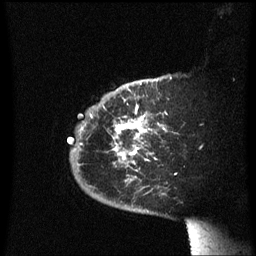
Breast MRI (dynamic contrast-enhanced), one sagittal slice. Position 48 of 60 along the scan axis. Dynamic contrast-enhanced series, image 2 of 3 at this slice position (ordered by acquisition). 1.5 T. TE 4.2 ms, TR 8.4 ms. 256 × 256 image matrix, field of view 200 × 200 mm. Patient: female, 38 years. Case-level facts recorded for this patient, not image findings: setting: breast cancer imaged before/during neoadjuvant chemotherapy; receptor status: HER2-positive.
Outlined on this slice (semi-automatic segmentation, software-assisted and operator-edited):
- analysis volume of interest (the breast-tissue region the enhancement analysis was run in; not a lesion): bounding box <67,78,179,213> (left, top, right, bottom; pixels)
- tumour enhancement mask (voxels above the 70 % enhancement threshold inside the analysis volume of interest): <81,84,149,163>